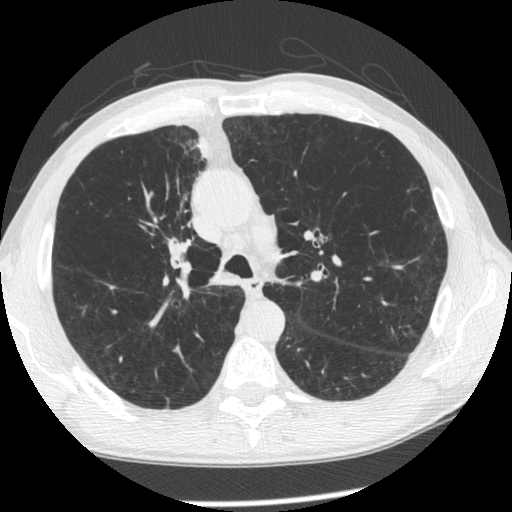
Low-dose screening chest CT, one axial slice; position 159 of 261 along the scan axis; reconstruction kernel STANDARD; lung window (W 1500 / L -600 HU); 512 × 512 image matrix, field of view 340 × 340 mm.
Annotated regions visible in this slice (expert manual segmentation):
- lesion 1 (tumor, upper lobe of right lung): bounding box <197,135,210,158> (left, top, right, bottom; pixels)